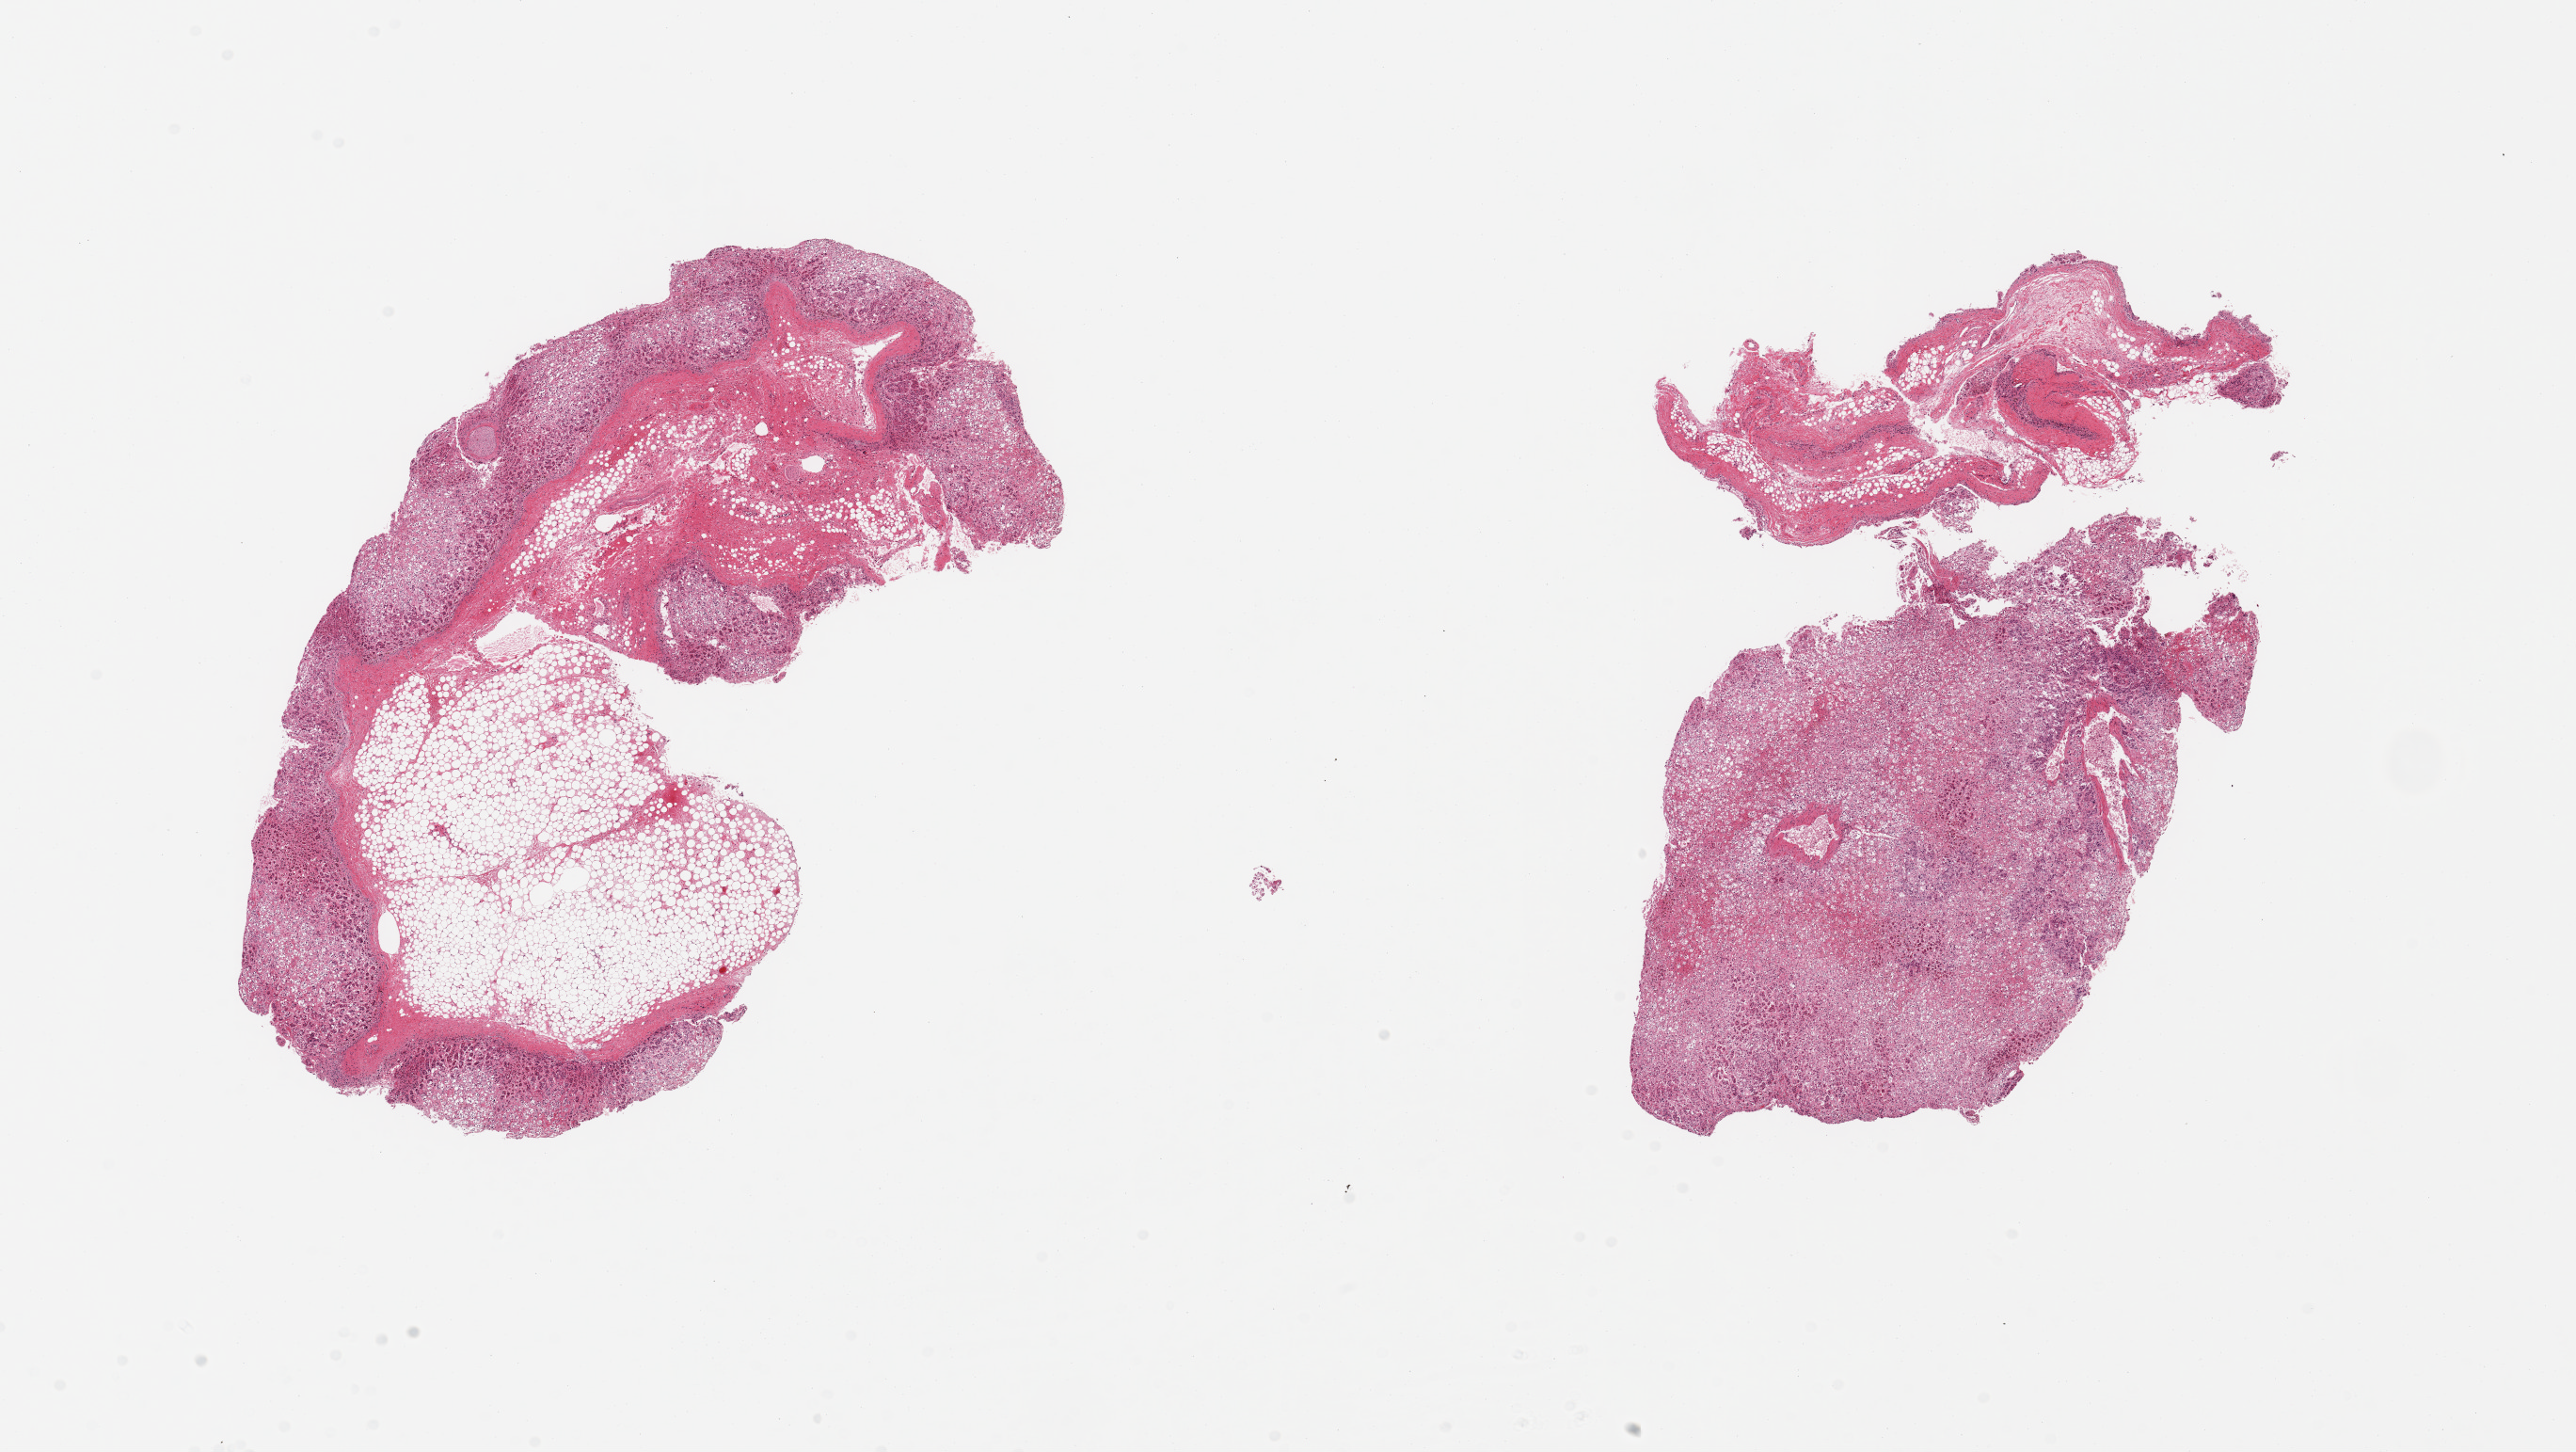
Digitized H&E-stained section, shown as a low-resolution overview of the whole scanned area (about 21.7 x 12.2 mm). PAXgene-fixed, paraffin-embedded tissue. Sampled site (target tissue): adrenal gland. Tissue donor sample. Donor sex: female.
Pathologist's review note for this sample: 2 pieces; 70% external fibrofatty content in 1, 40% in other (26 black may have been trimmed).